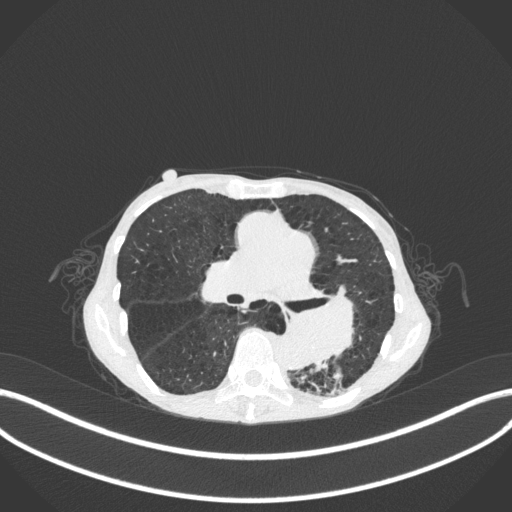
Chest CT, one axial slice; position 155 of 347 along the scan axis; reconstruction kernel B31f; 120 kVp; lung window (W 1500 / L -600 HU); 1 mm slice thickness; 512 × 512 image matrix, field of view 400 × 400 mm. Female patient, age 70 years. Case-level facts recorded for this patient, not image findings: clinical TNM (as recorded): T3 N0 M0; histopathological grade: G3.
Structures marked on this image (rectangle marked by the reading radiologist):
- lung tumour (recorded histology: small cell carcinoma): bounding box <283,285,365,366> (left, top, right, bottom; pixels)